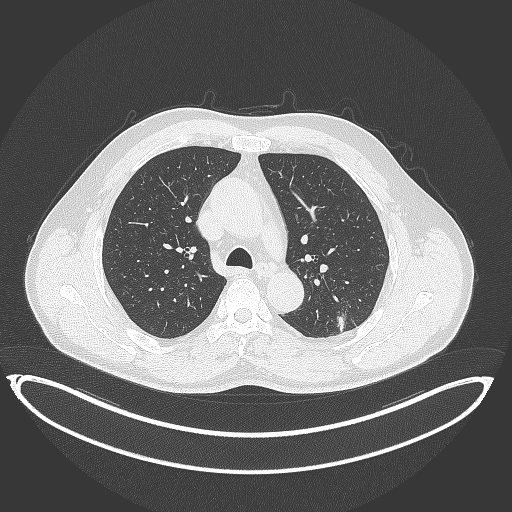
Chest CT, one axial slice. Slice 242 of 399 in the series (ordered by position). 120 kVp. Lung window (W 1500 / L -600 HU). 1 mm slice thickness. 512 × 512 image matrix, field of view 469 × 469 mm. Patient: male, 58 years. Case-level facts recorded for this patient, not image findings: clinical TNM (as recorded): T1c N0 M0; histopathological grade: G1-2.
Structures marked on this image (bounding box drawn by a radiologist):
- lung tumour (recorded histology: adenocarcinoma): bounding box <333,310,353,336> (left, top, right, bottom; pixels)